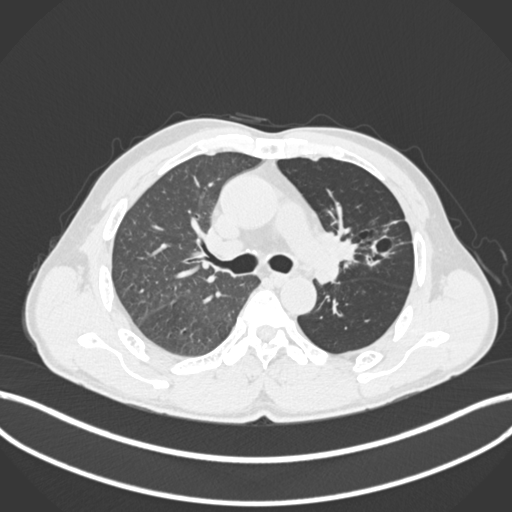
Chest CT, one axial slice. Slice 121 of 255 in the series (ordered by position). Reconstruction kernel B30f. 120 kVp. Lung window (W 1500 / L -600 HU). 1 mm slice thickness. 512 × 512 image matrix, field of view 400 × 400 mm. Male patient, age 57 years. Case-level facts recorded for this patient, not image findings: clinical TNM (as recorded): T2b N0 M0.
Outlined on this slice (rectangle marked by the reading radiologist):
- lung tumour (recorded histology: squamous cell carcinoma): bounding box [x1, y1, x2, y2] px = [318, 225, 369, 264]